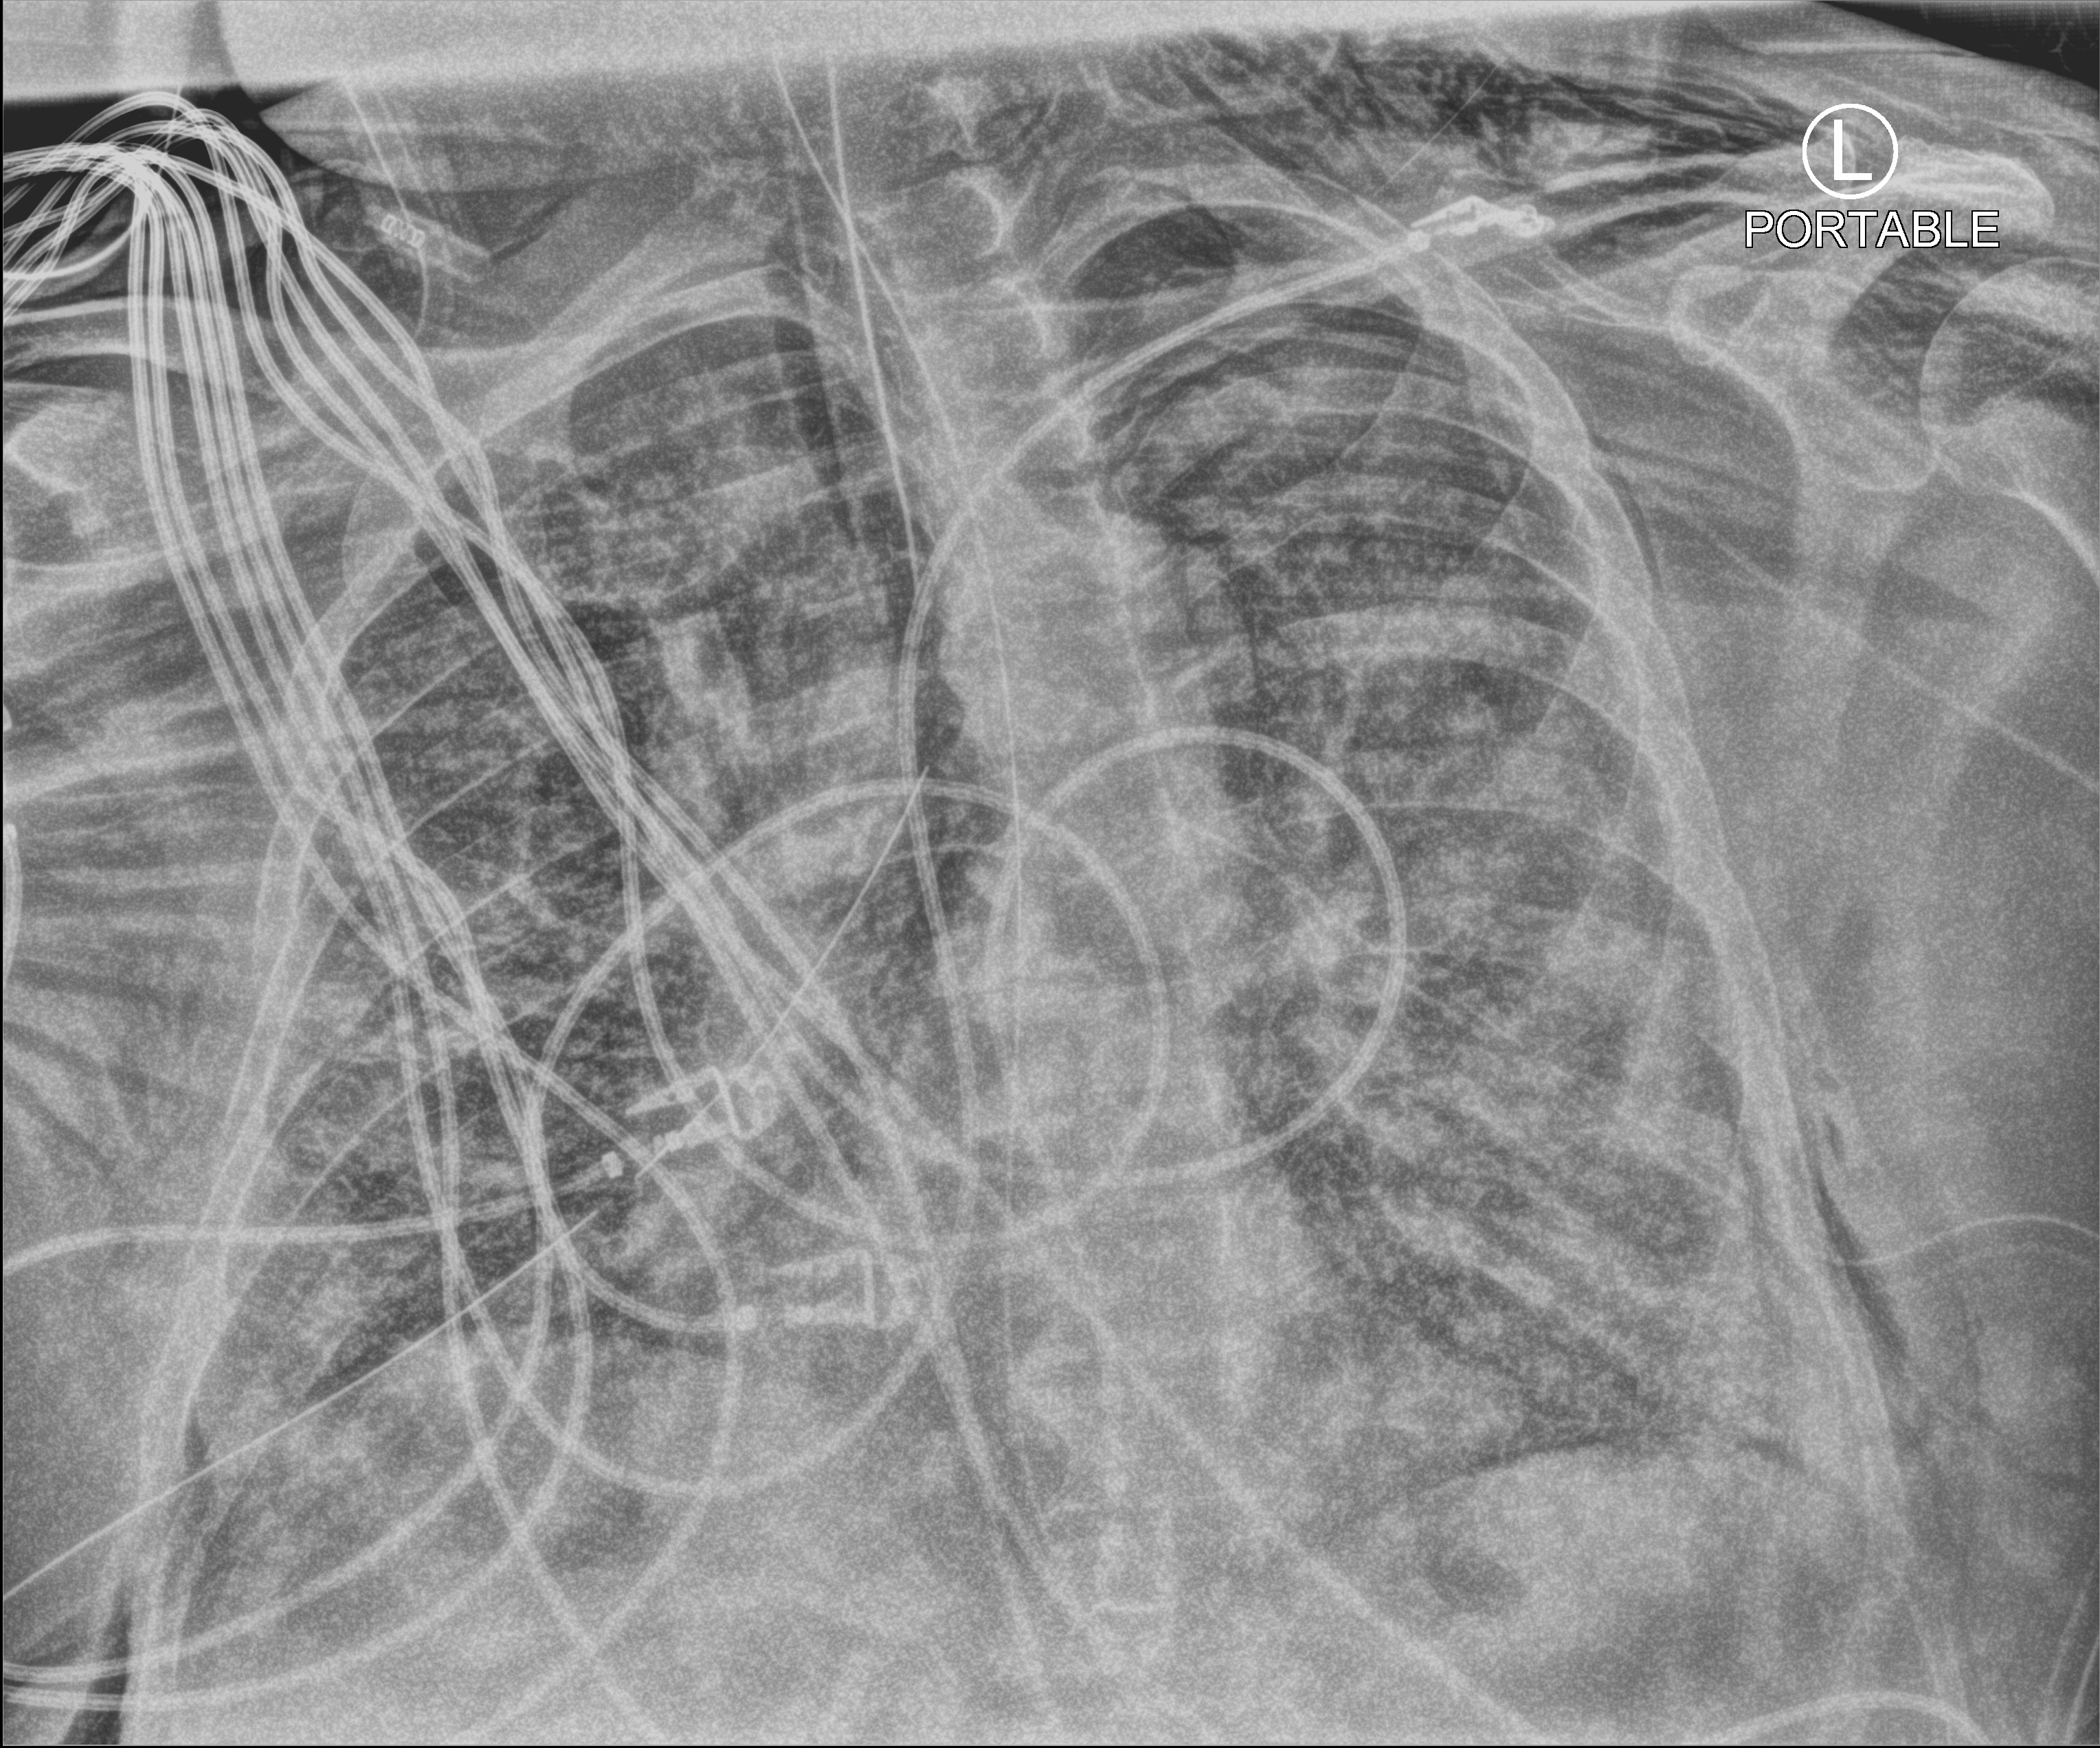
Portable chest radiograph, anteroposterior (AP) projection. Patient hospitalised with COVID-19, aged 18–59 years.
Admission-level facts for this patient (not findings on this image; timing relative to this image not recorded):
- admitted to intensive care during this hospital stay: yes
- COPD (admission record): no